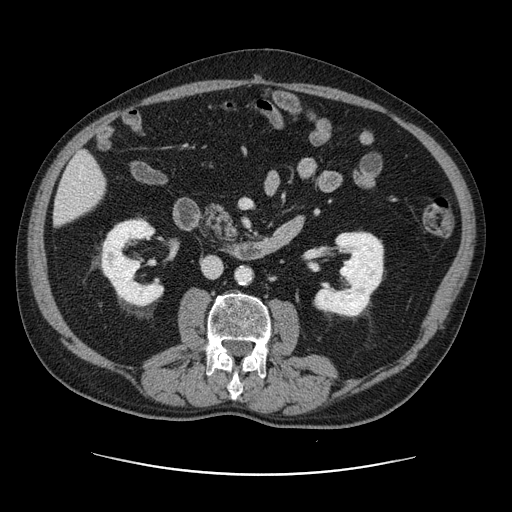
Contrast-enhanced abdominal CT, one axial slice; position 36 of 141 along the scan axis; intravenous contrast given; soft-tissue window (W 400 / L 40 HU); 2.5 mm slice thickness; 512 × 512 image matrix, field of view 395 × 395 mm. Male patient, age 72 years. From the clinical record (not read from this slice): diagnosis: colorectal cancer liver metastases, imaged before liver resection; multiple liver metastases: yes; largest metastasis: 5.4 cm; disease in both lobes: yes.
Outlined on this slice (outlined manually by an expert reader):
- liver: bounding box <54,153,106,225> (left, top, right, bottom; pixels)
- planned liver remnant (the part of the liver to remain after resection): <54,153,106,225>